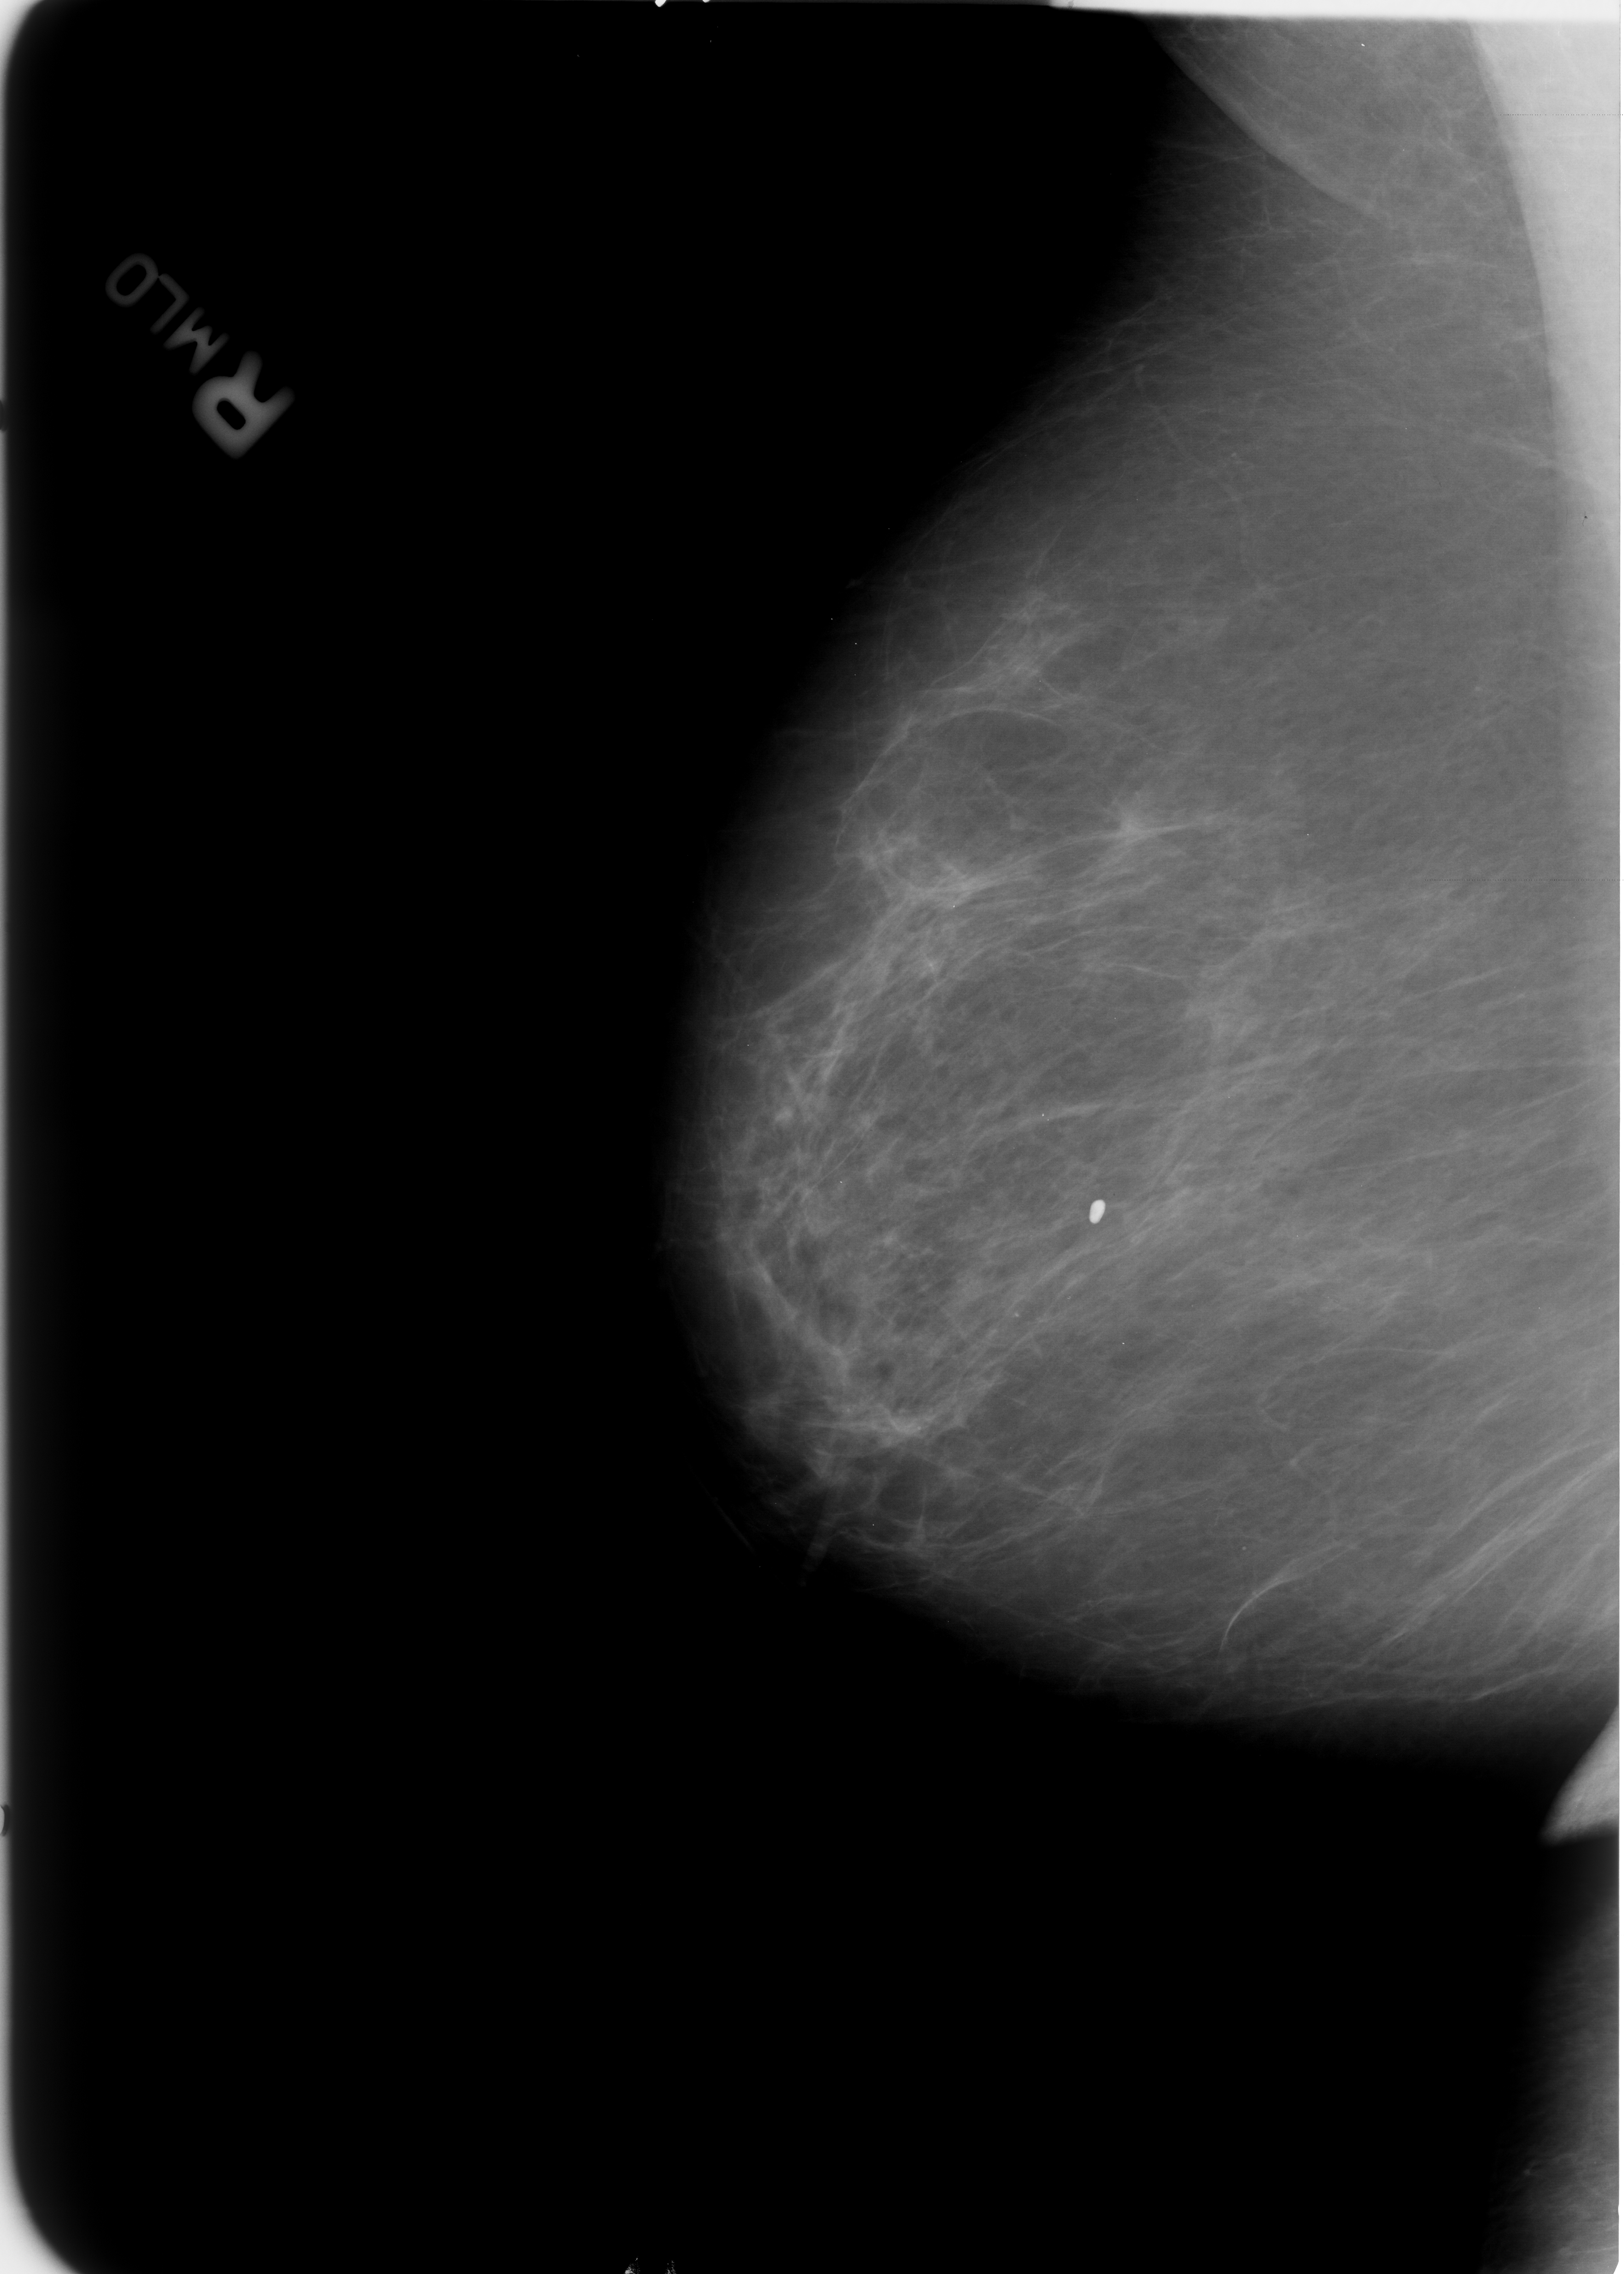
Digitized screen-film mammogram; right breast; mediolateral oblique (MLO) view; breast composition: almost entirely fatty (BI-RADS density category 1 of 4).
Radiologist-marked abnormalities on this image: calcifications, morphology coarse; BI-RADS assessment category 2; benign; no additional work-up was recommended (benign without callback).